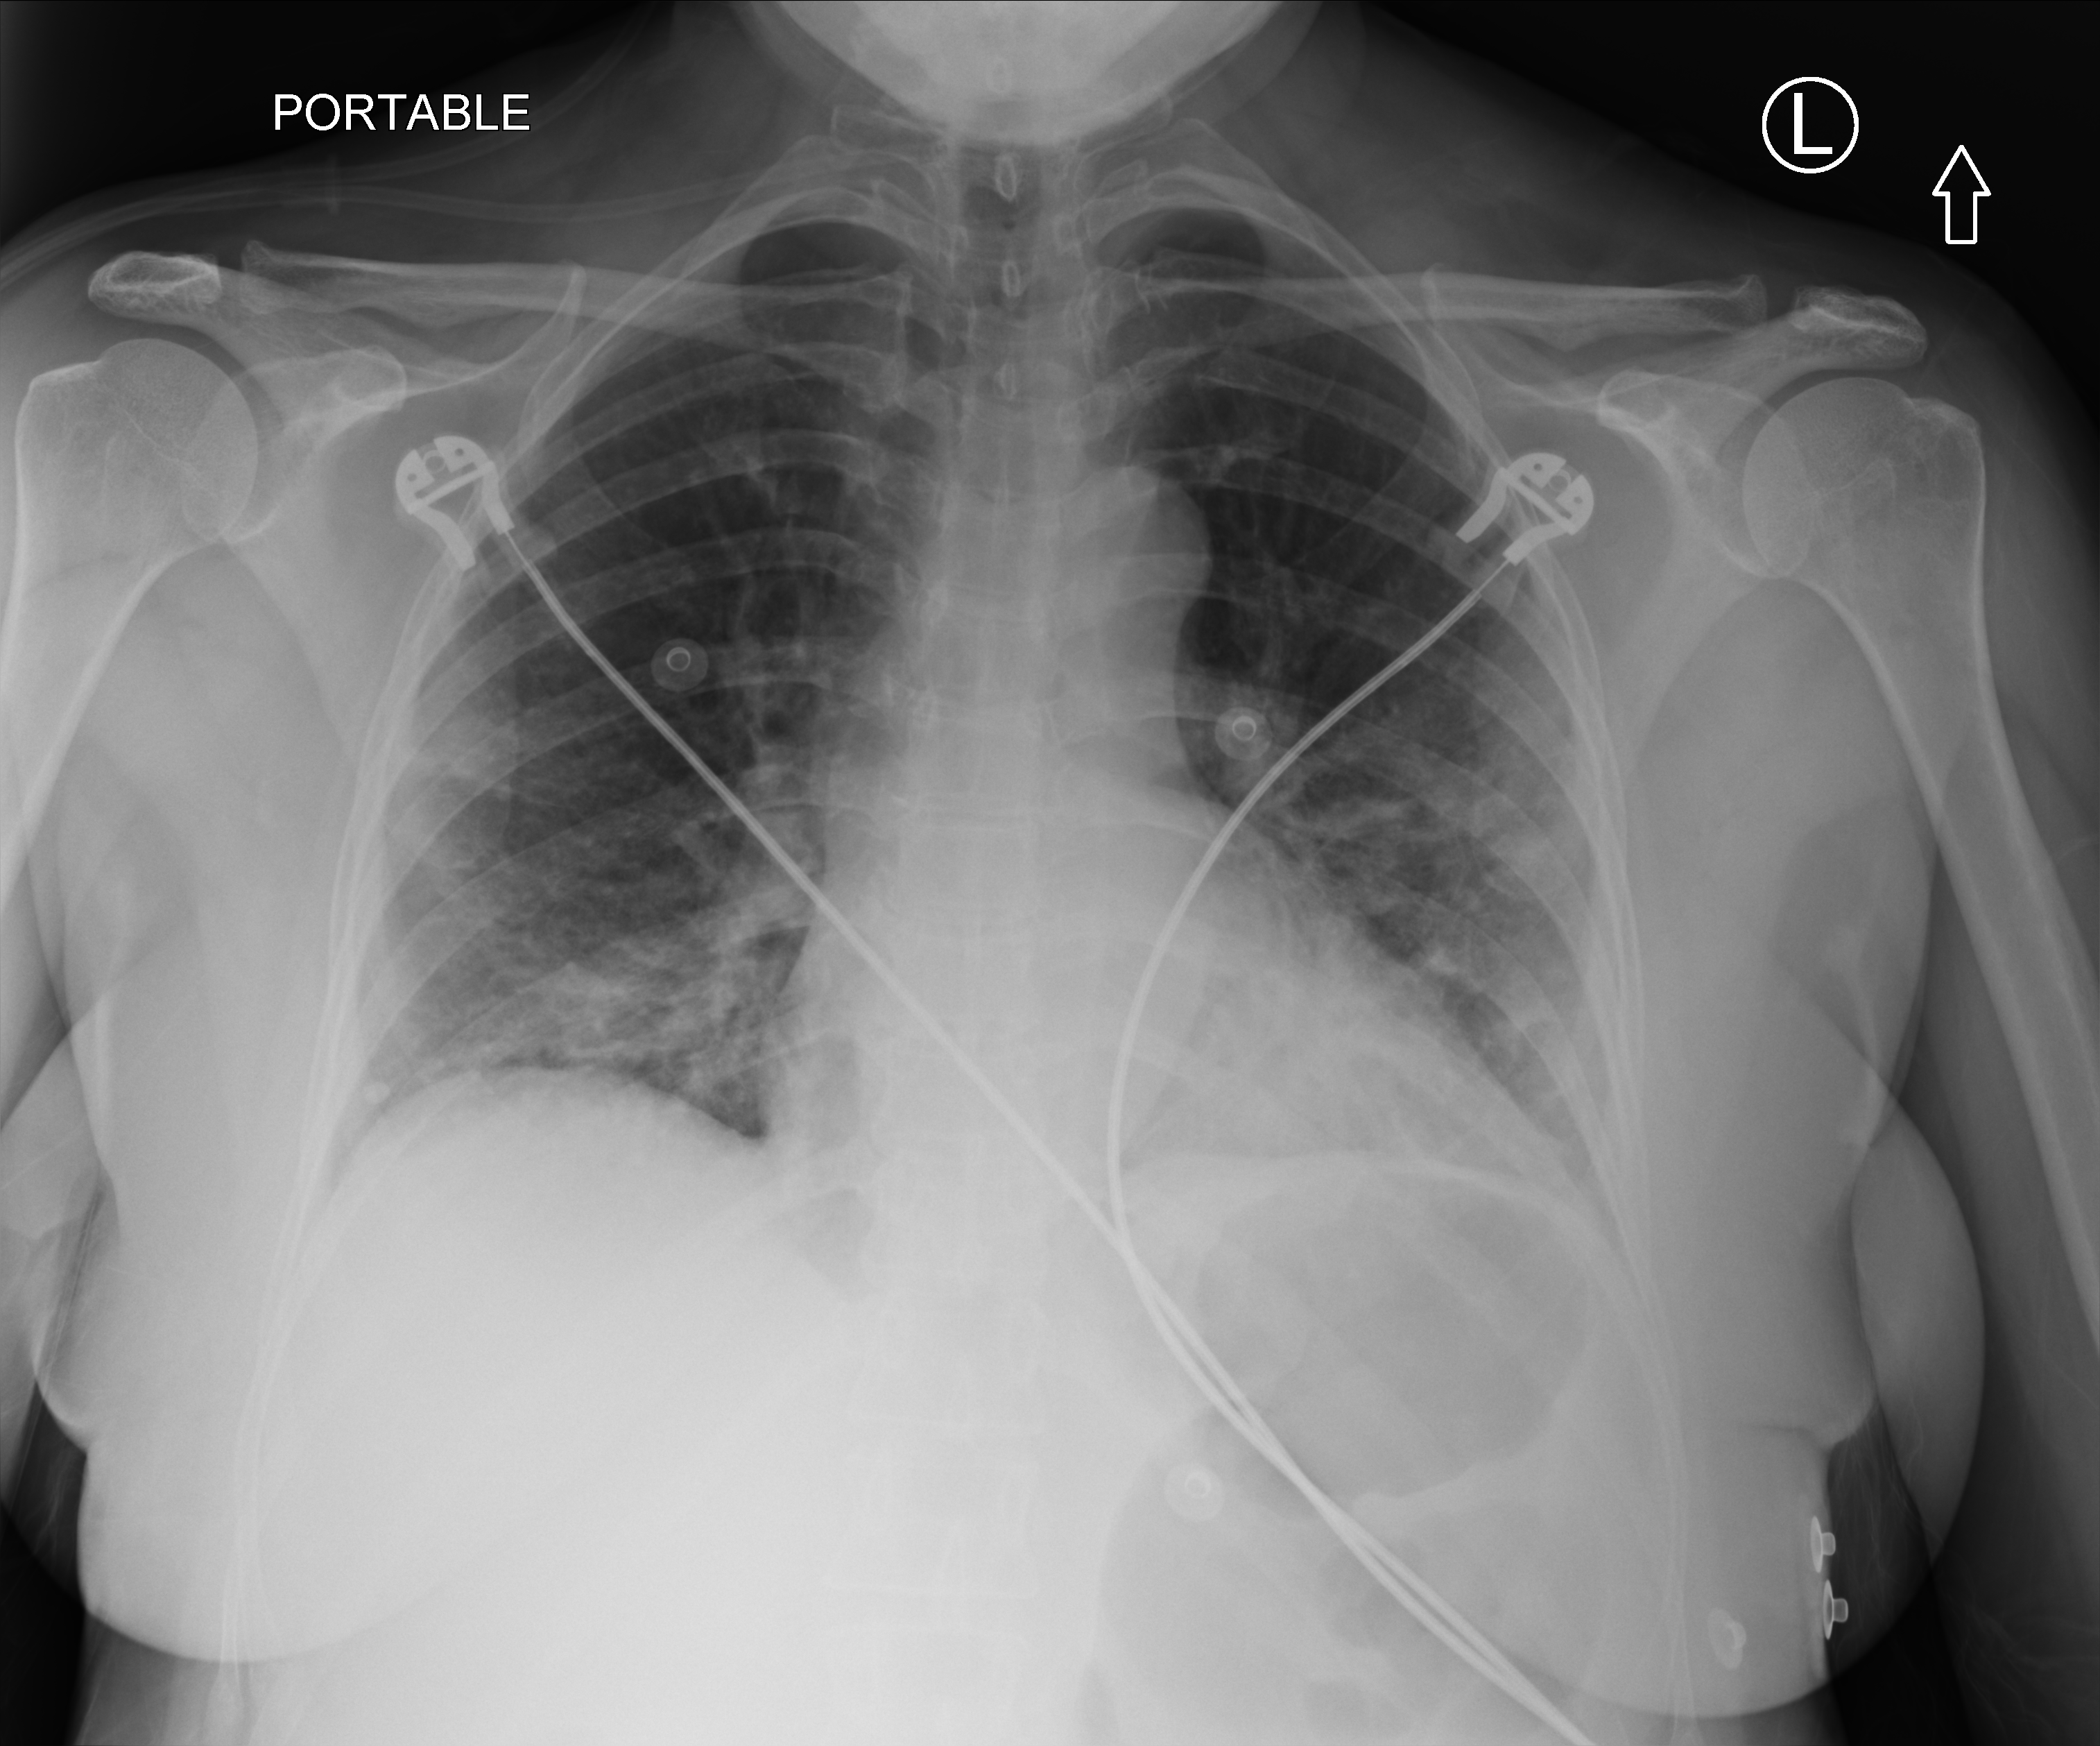
Portable chest radiograph; anteroposterior (AP) projection. Female patient hospitalised with COVID-19, age 60–74 years.
Hospital-stay facts (about this admission, not read from this image; timing relative to this image not recorded): admitted to intensive care during this hospital stay: no; mechanically ventilated during this hospital stay: no.